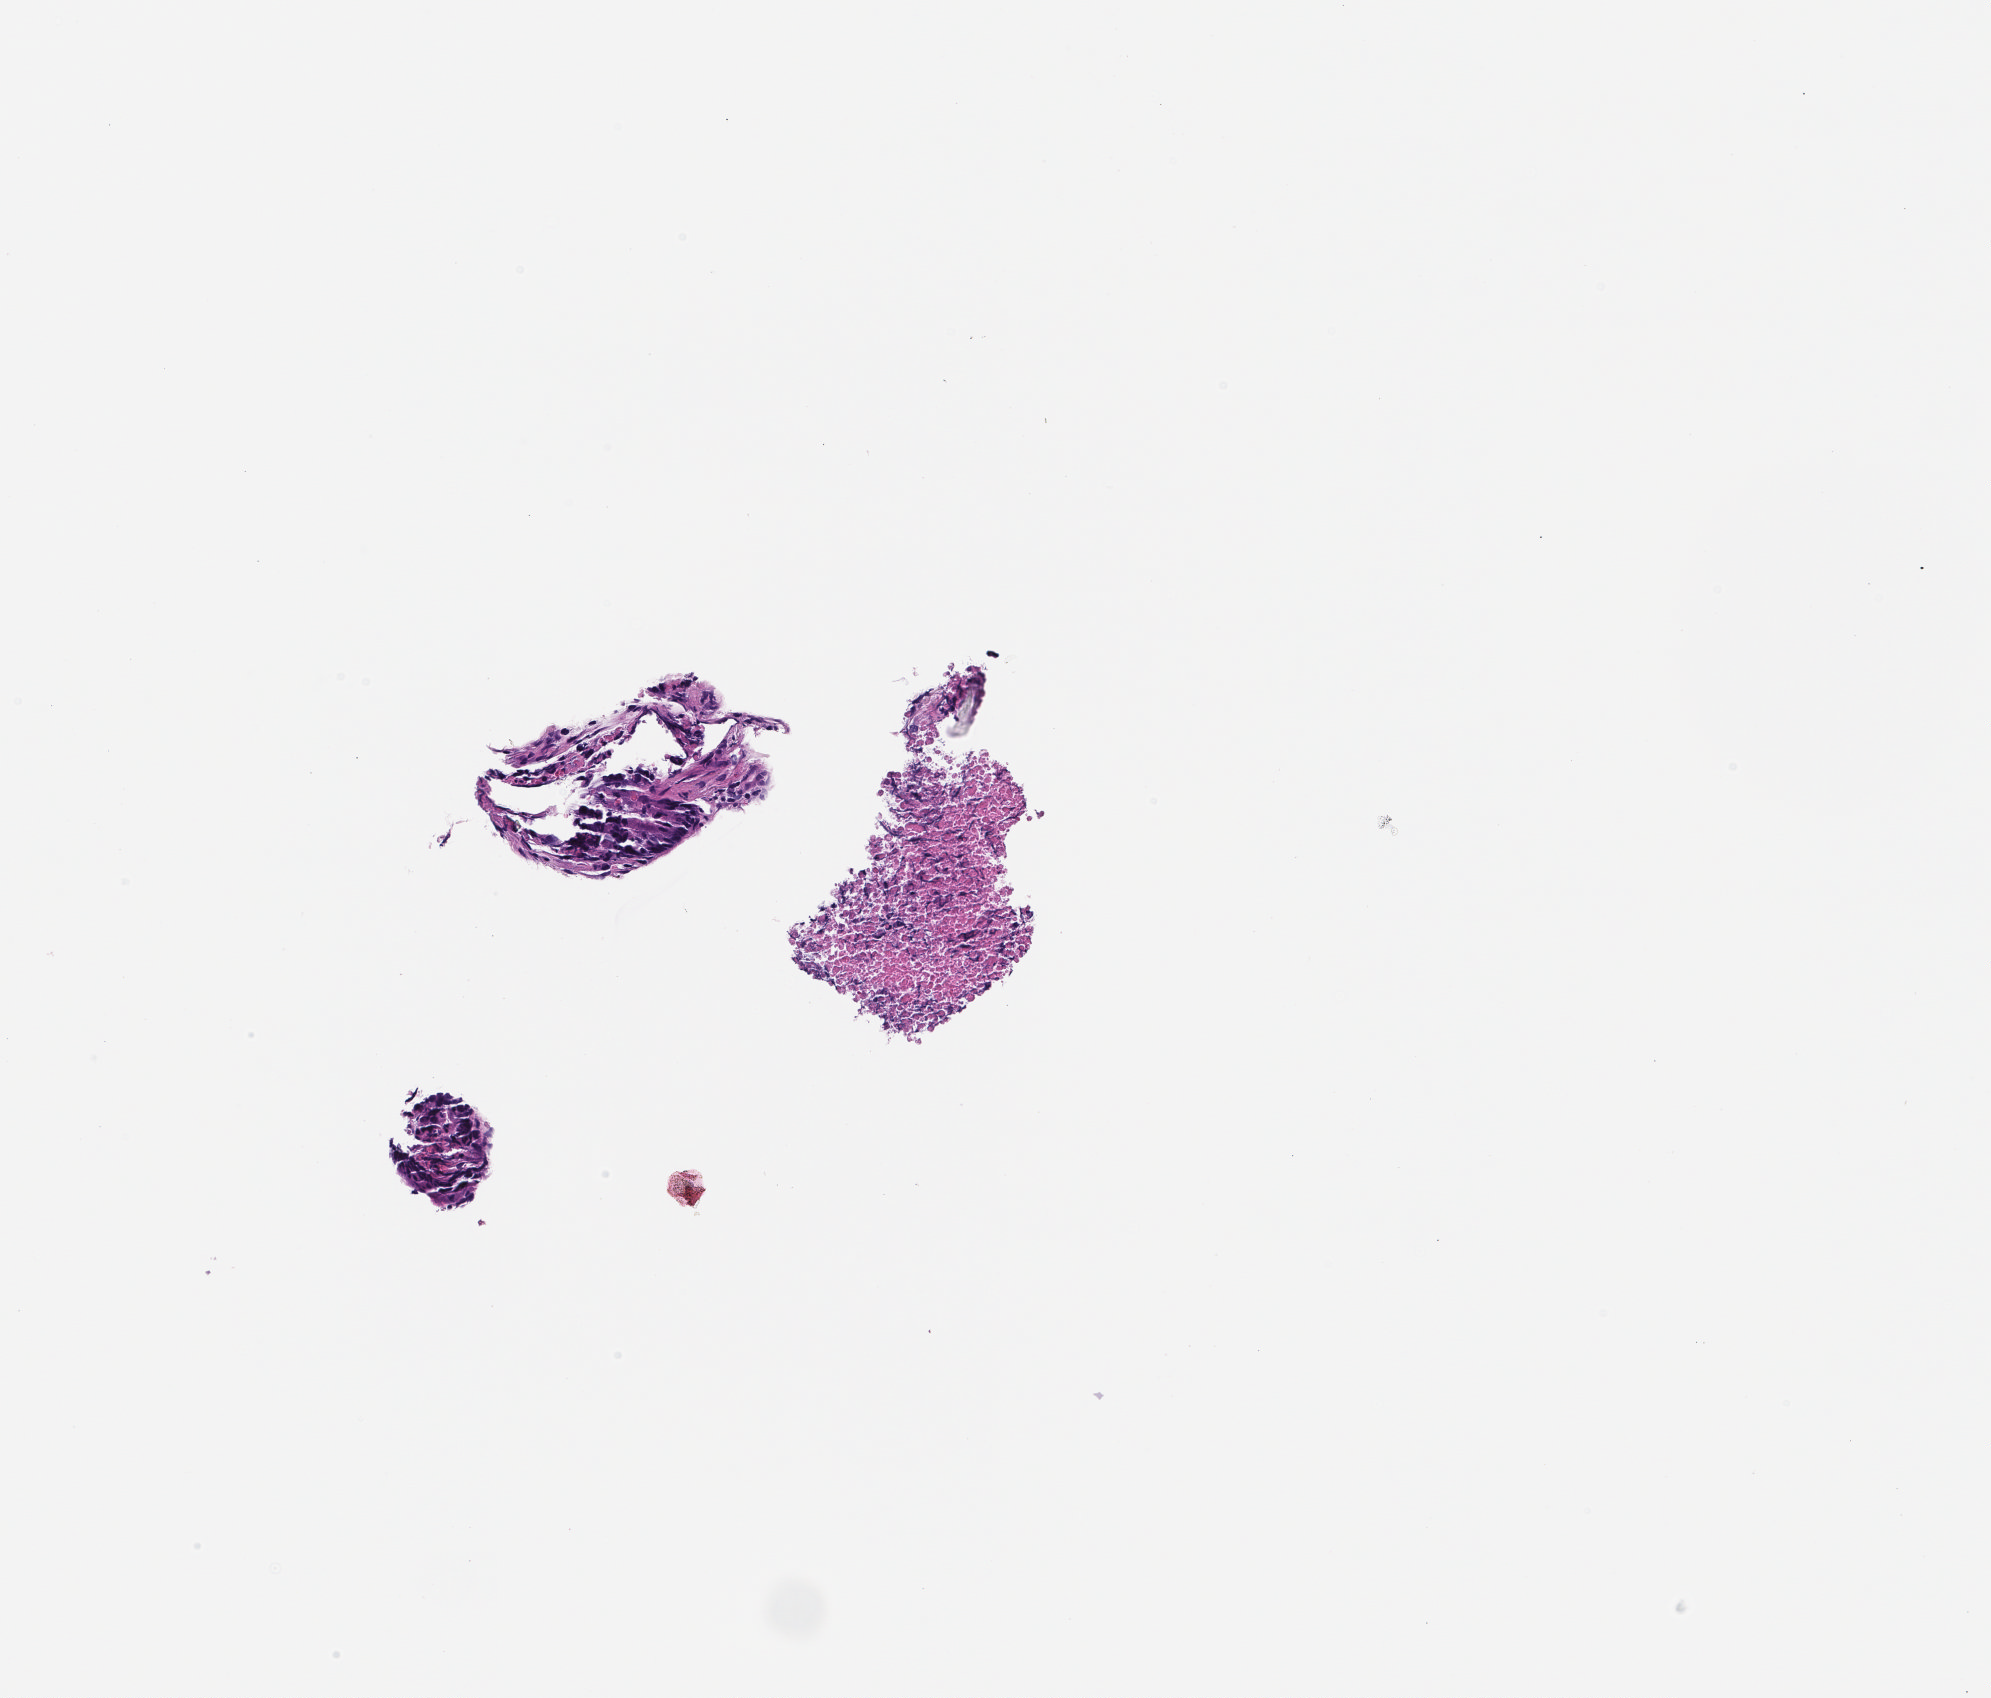
Digitized haematoxylin and eosin-stained section — a low-resolution overview of the entire scanned area, about 2.0 x 1.7 mm, FFPE section, collected at baseline (before treatment). Patient sex: male.
• this section: metastatic tumor tissue
• patient diagnosis (primary): Colorectal Carcinoma